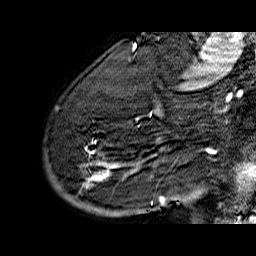
Breast MRI (dynamic contrast-enhanced), one sagittal slice; dynamic contrast-enhanced series, time point 2 of 6 at this slice position (early post-contrast); 1.5 T; TE 6.5 ms, TR 32.9 ms; 4 mm slice thickness; 256 × 256 image matrix, field of view 200 × 200 mm. Female patient. From the clinical record (not read from this slice): setting: breast cancer imaged before/during neoadjuvant chemotherapy; receptor status: HR-positive, HER2-negative.
Annotated regions visible in this slice (semi-automatically segmented with operator editing):
- analysis volume of interest (the breast-tissue region the enhancement analysis was run in; not a lesion): box from (x=45, y=74) to (x=176, y=210) px
- tumour enhancement mask (voxels above the 100 % enhancement threshold inside the analysis volume of interest): (x=79, y=111)–(x=164, y=202)